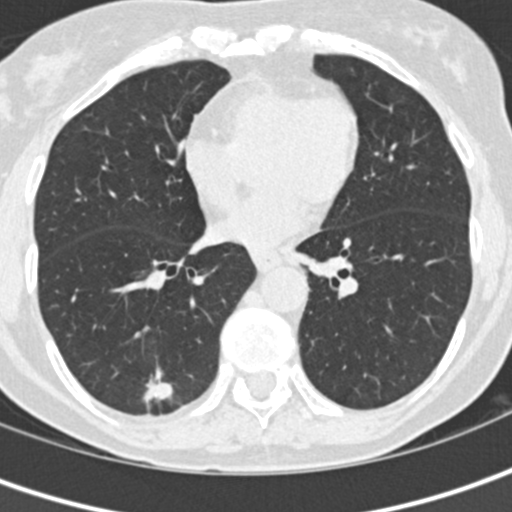
Low-dose screening chest CT, one axial slice; position 64 of 152 along the scan axis; reconstruction kernel B30f; lung window (W 1500 / L -600 HU); 2 mm slice thickness; 512 × 512 image matrix, field of view 280 × 280 mm.
Annotated regions visible in this slice (outlined manually by an expert reader):
- lesion 1 (tumor, lower lobe of right lung): box from (x=143, y=366) to (x=173, y=405) px